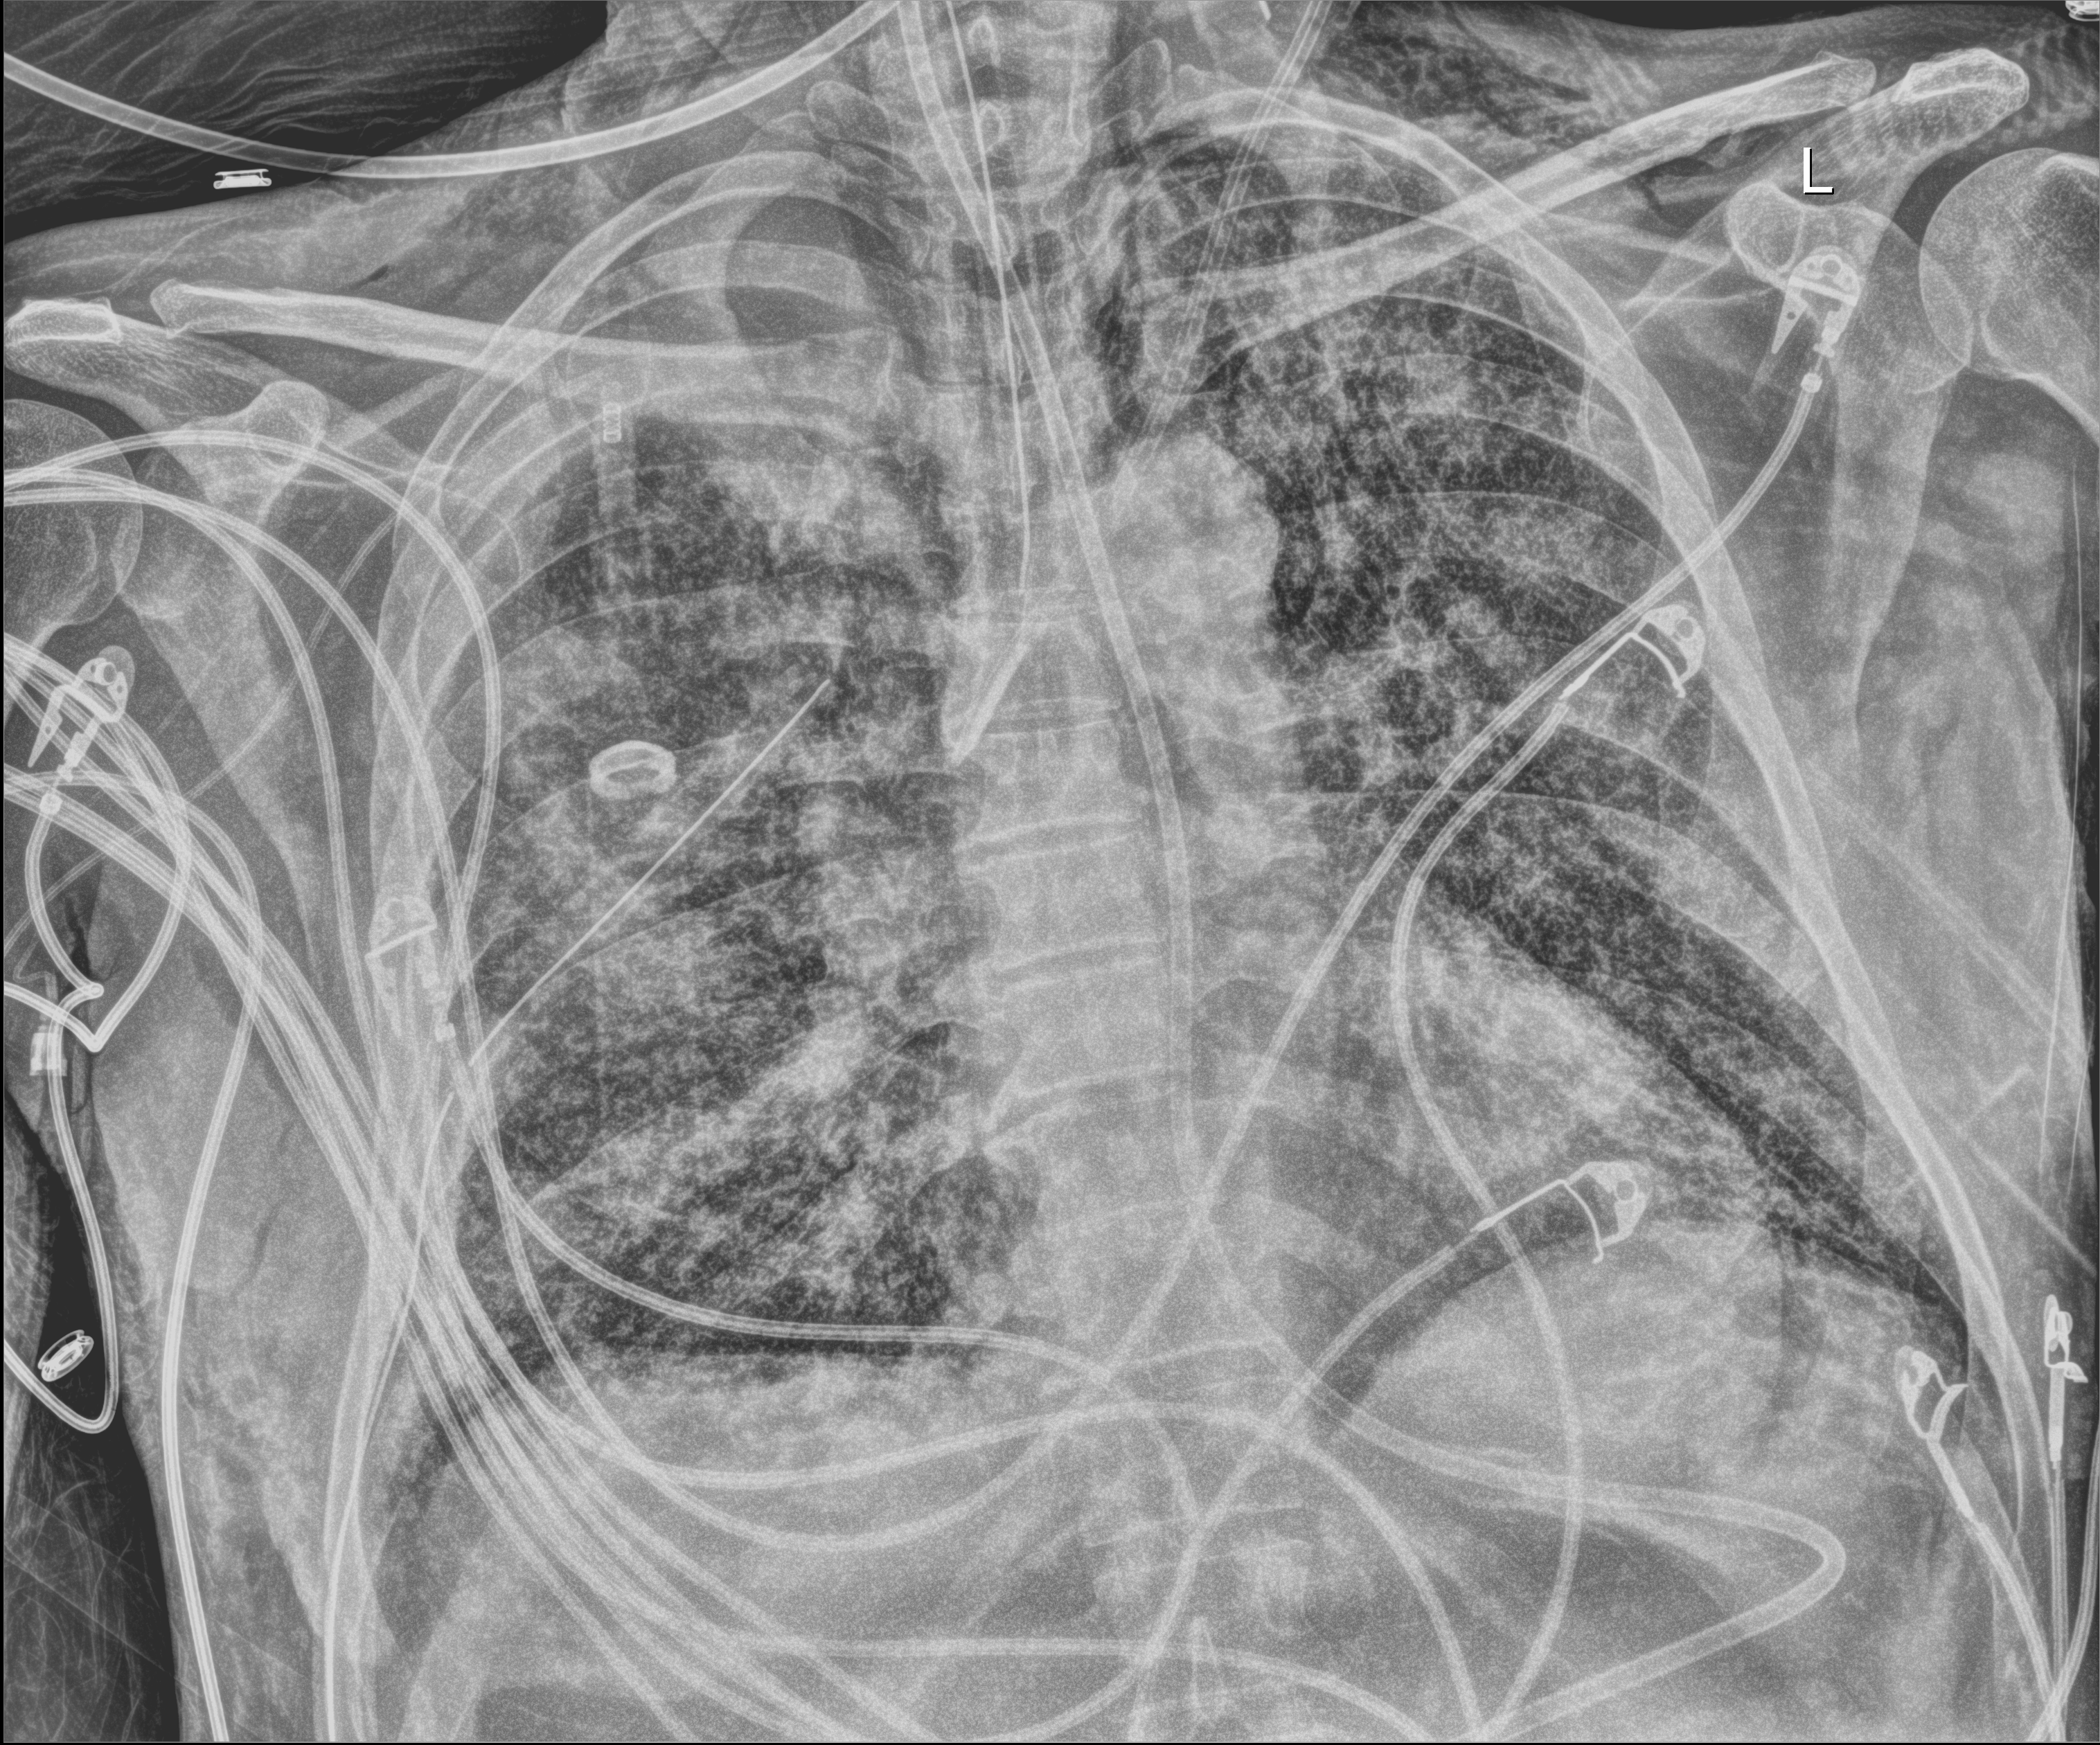
Bedside chest radiograph (digital radiography); anteroposterior (AP) projection. Patient hospitalised with COVID-19; male, aged 18–59 years.
From the hospital-stay record, not from the radiograph (when in the stay this image was taken is not recorded): length of hospital stay: 42 days; admitted to intensive care during this hospital stay: yes; mechanically ventilated during this hospital stay: yes.